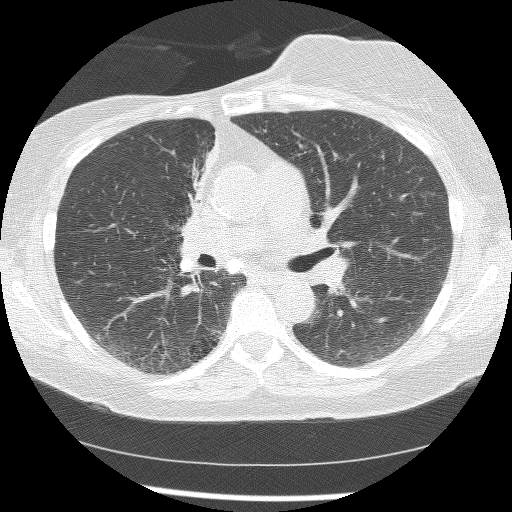
Low-dose screening chest CT, axial slice. First (baseline) screen. Lung window (W 1500 / L -600 HU). 2.5 mm slice thickness. Slice 67 of 172 in the series. 512 × 512 image matrix. Female participant, aged 56 years at enrolment.
• Lesion marked by an expert reader, bounding box (x1, y1, x2, y2) in pixels: (160, 132, 214, 253).
• The screening reader recorded 2 non-calcified nodules or masses ≥4 mm on this exam; which of them this box marks is not recorded.
• Lung cancer was diagnosed 1185 days after this screen: adenocarcinoma, NOS, right upper lobe, stage IIIB (AJCC 6th edition), 8 mm at pathology.